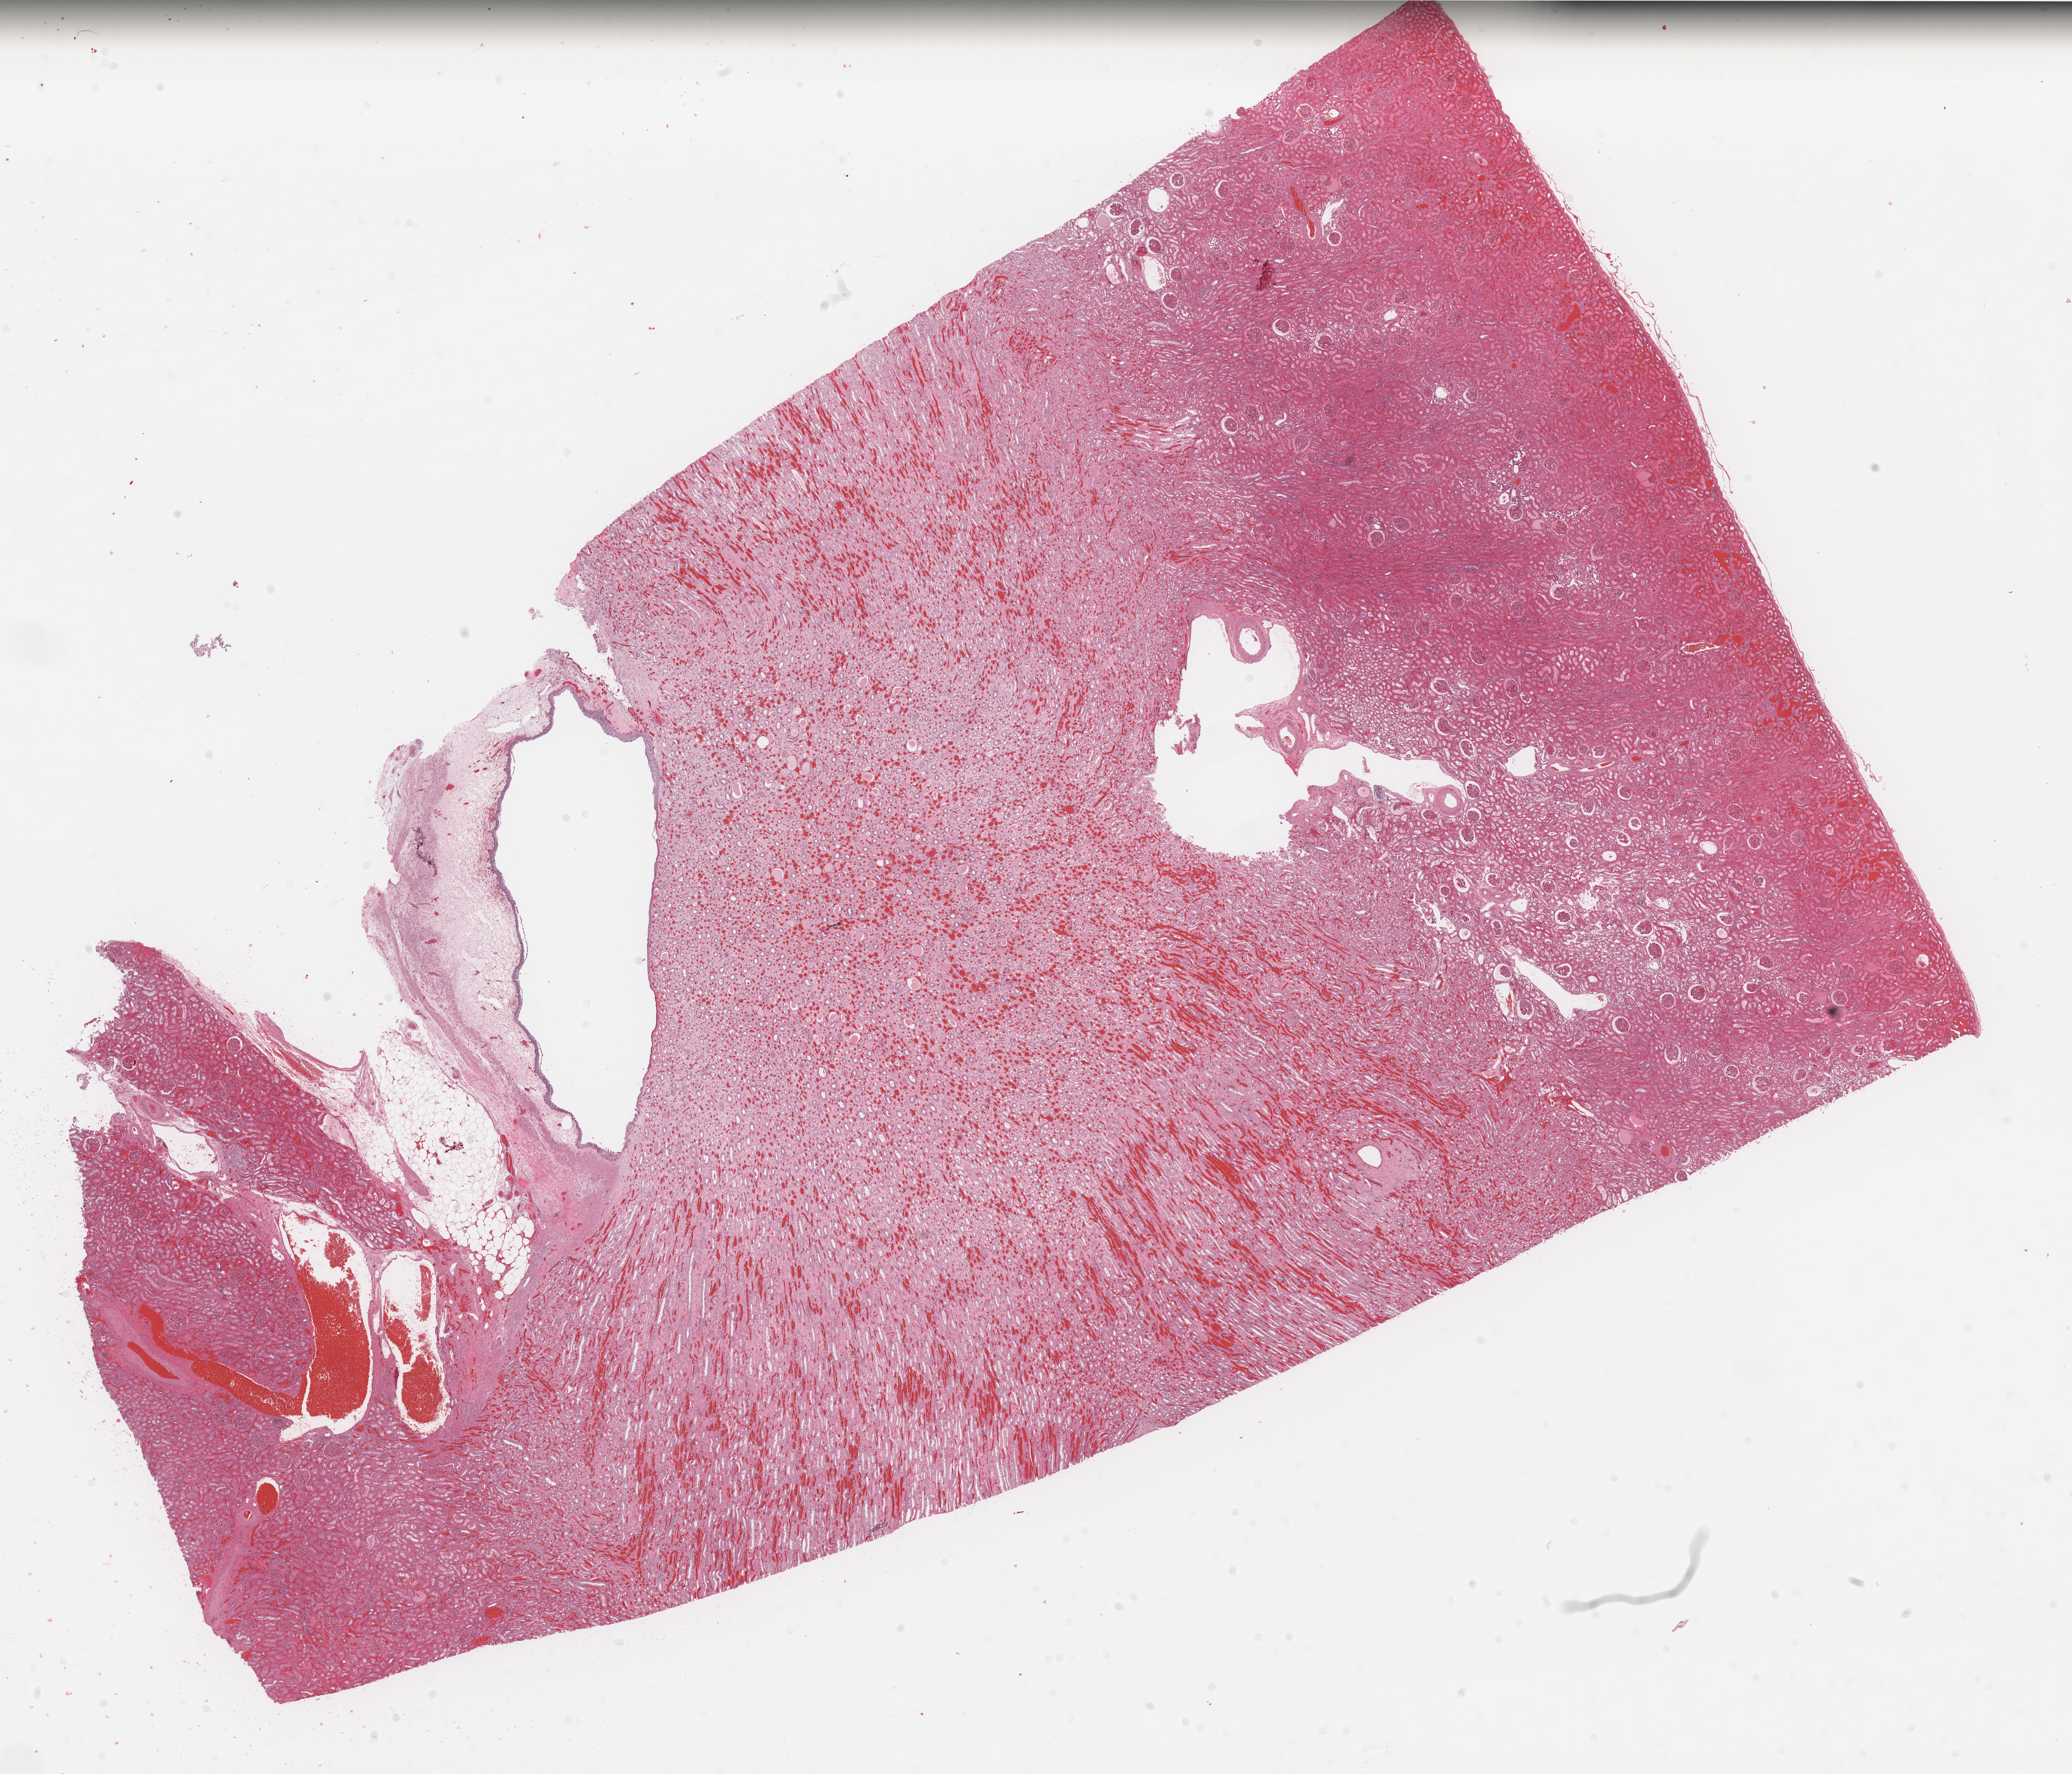
Digitized H&E tissue section (whole slide), whole scanned area (about 26.8 x 23.0 mm, slide scanned at 40x) shown as a low-resolution overview. Formalin-fixed paraffin-embedded (FFPE) diagnostic section. Primary tumour sample from the kidney. Female, age 52 years at initial diagnosis. Slide review estimates, as recorded: tumour cells 70%, tumour nuclei 70%, normal cells 0%, stromal cells 30%, necrosis 0%. Inflammatory infiltration, as recorded: lymphocyte infiltration 3%, monocyte infiltration 1%, neutrophil infiltration 1%.
AJCC pathologic stage: III (6th edition). Pathologic diagnosis: Renal cell carcinoma, chromophobe type.